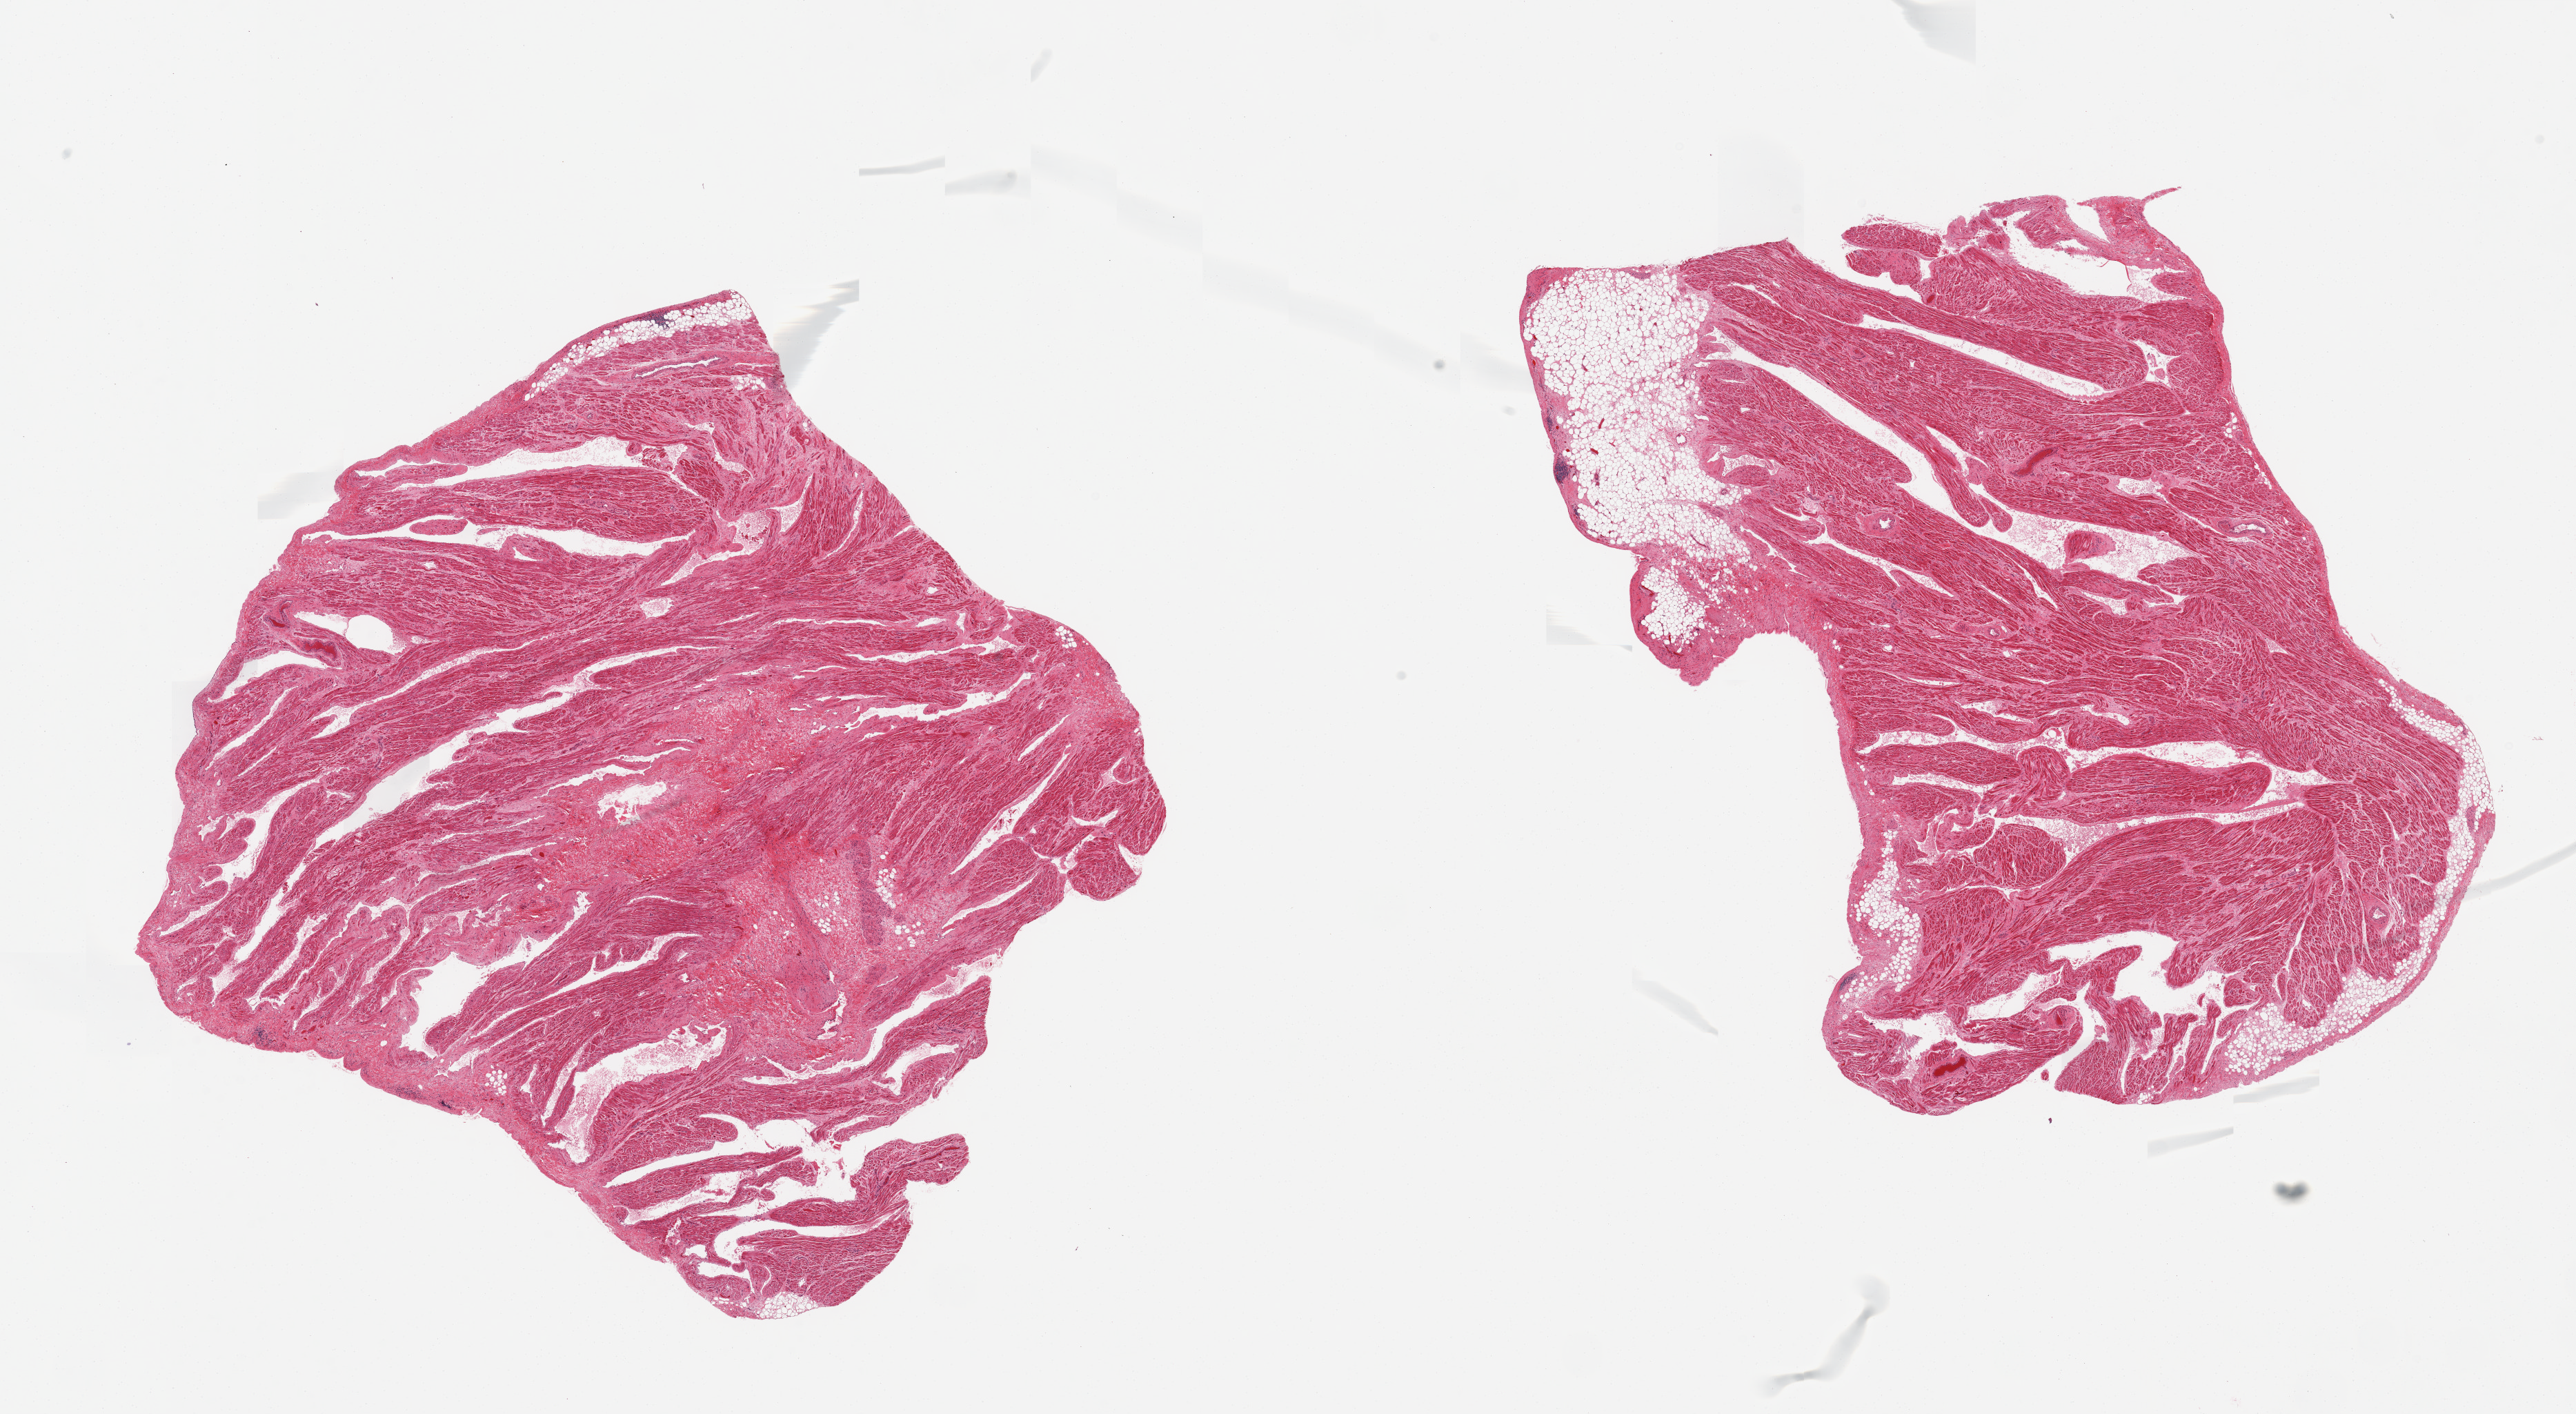
Digitized hematoxylin and eosin (H&E)-stained section, brightfield — a low-resolution overview of the entire scanned area, about 29.5 x 16.2 mm (slide scanned at 20x). PAXgene-fixed, paraffin-embedded tissue. Sampled site (target tissue): auricular appendage. Donor tissue sample. Male donor.
Review note (as recorded): 2 pieces; atrial appendage with interstitial fibrosis and 10% fat.